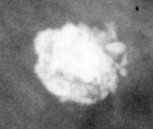
Crop from a digitized film mammogram around one marked abnormality, left breast, MLO view.
Marked abnormality: calcifications, distribution linear; BI-RADS assessment category 2; subtlety rating 3 on a 1 (subtle) to 5 (obvious) scale; benign without callback (not worked up further).